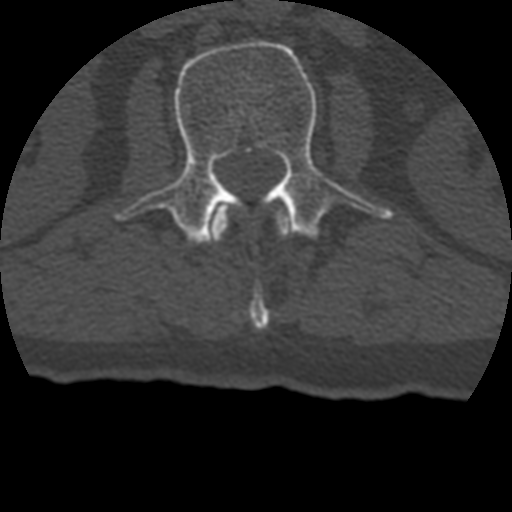
CT including the spine, one axial slice; slice 122 of 399 in the series (ordered by position); reconstruction kernel STANDARD; 120 kVp; bone window (W 1800 / L 400 HU); 1.25 mm slice thickness; 512 × 512 image matrix, field of view 160 × 160 mm. Patient age 69 years. From the clinical record (not read from this slice): primary cancer: prostate.
Annotated regions visible in this slice (semi-automatic segmentation, software-assisted and operator-edited):
- L1 vertebra: bounding box (x1, y1, x2, y2) in pixels: (210, 201, 293, 329)
- L2 vertebra: (113, 40, 394, 244)